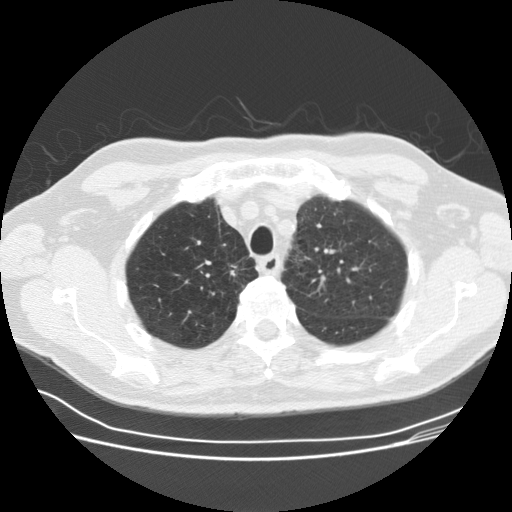
Low-dose screening chest CT, axial slice; third screening round (two years after baseline); lung window (W 1500 / L -600 HU); 120 kVp. Male, age 69 years at enrolment. Current smoker at enrolment.
Lesion marked by an expert reader, box from (x=219, y=256) to (x=255, y=291) px. The exam's reader record, not a measurement of the box and not confirmed to be the same lesion: non-calcified nodule or mass ≥4 mm, right upper lobe, 12 × 10 mm, spiculated (stellate) margins, soft tissue attenuation, pre-existing on the prior screen: yes; interval growth: yes. Participant outcome: lung cancer diagnosed 36 days after this screen — squamous cell carcinoma, NOS, right upper lobe, moderately differentiated (G2), stage IA (AJCC 6th edition), 9 mm at pathology.